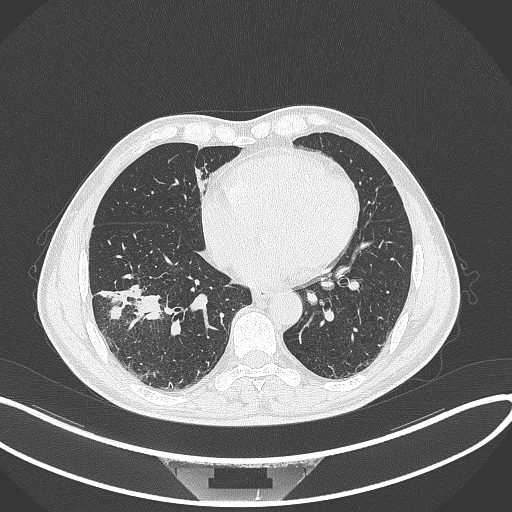
Chest CT, one axial slice. Slice 134 of 364 in the series (ordered by position). Reconstruction kernel B70f. 120 kVp. Lung window (W 1500 / L -600 HU). 1 mm slice thickness. 512 × 512 image matrix, field of view 400 × 400 mm. Patient: male, 58 years. From the clinical record (not read from this slice): clinical TNM (as recorded): T3 N0 M0; histopathological grade: G2.
Annotated regions visible in this slice (rectangle marked by the reading radiologist):
- lung tumour (recorded histology: squamous cell carcinoma): bounding box [x1, y1, x2, y2] px = [105, 282, 161, 321]